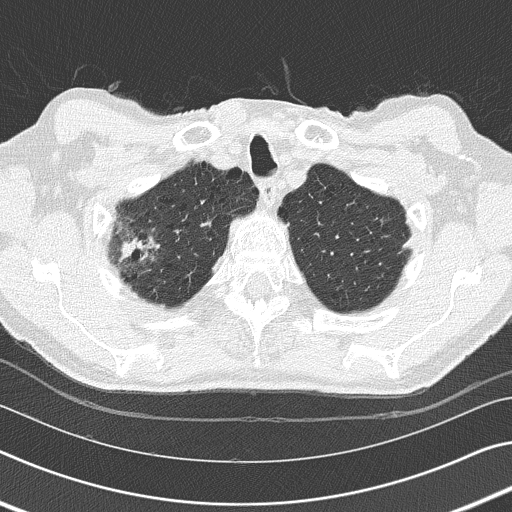
Low-dose screening chest CT, one axial slice. Position 141 of 155 along the scan axis. 120 kVp. Lung window (W 1500 / L -600 HU). 2 mm slice thickness. 512 × 512 image matrix, field of view 340 × 340 mm.
Outlined on this slice (outlined manually by an expert reader):
- lesion 1 (tumor, middle lobe of right lung): bounding box [x1, y1, x2, y2] px = [113, 236, 160, 266]